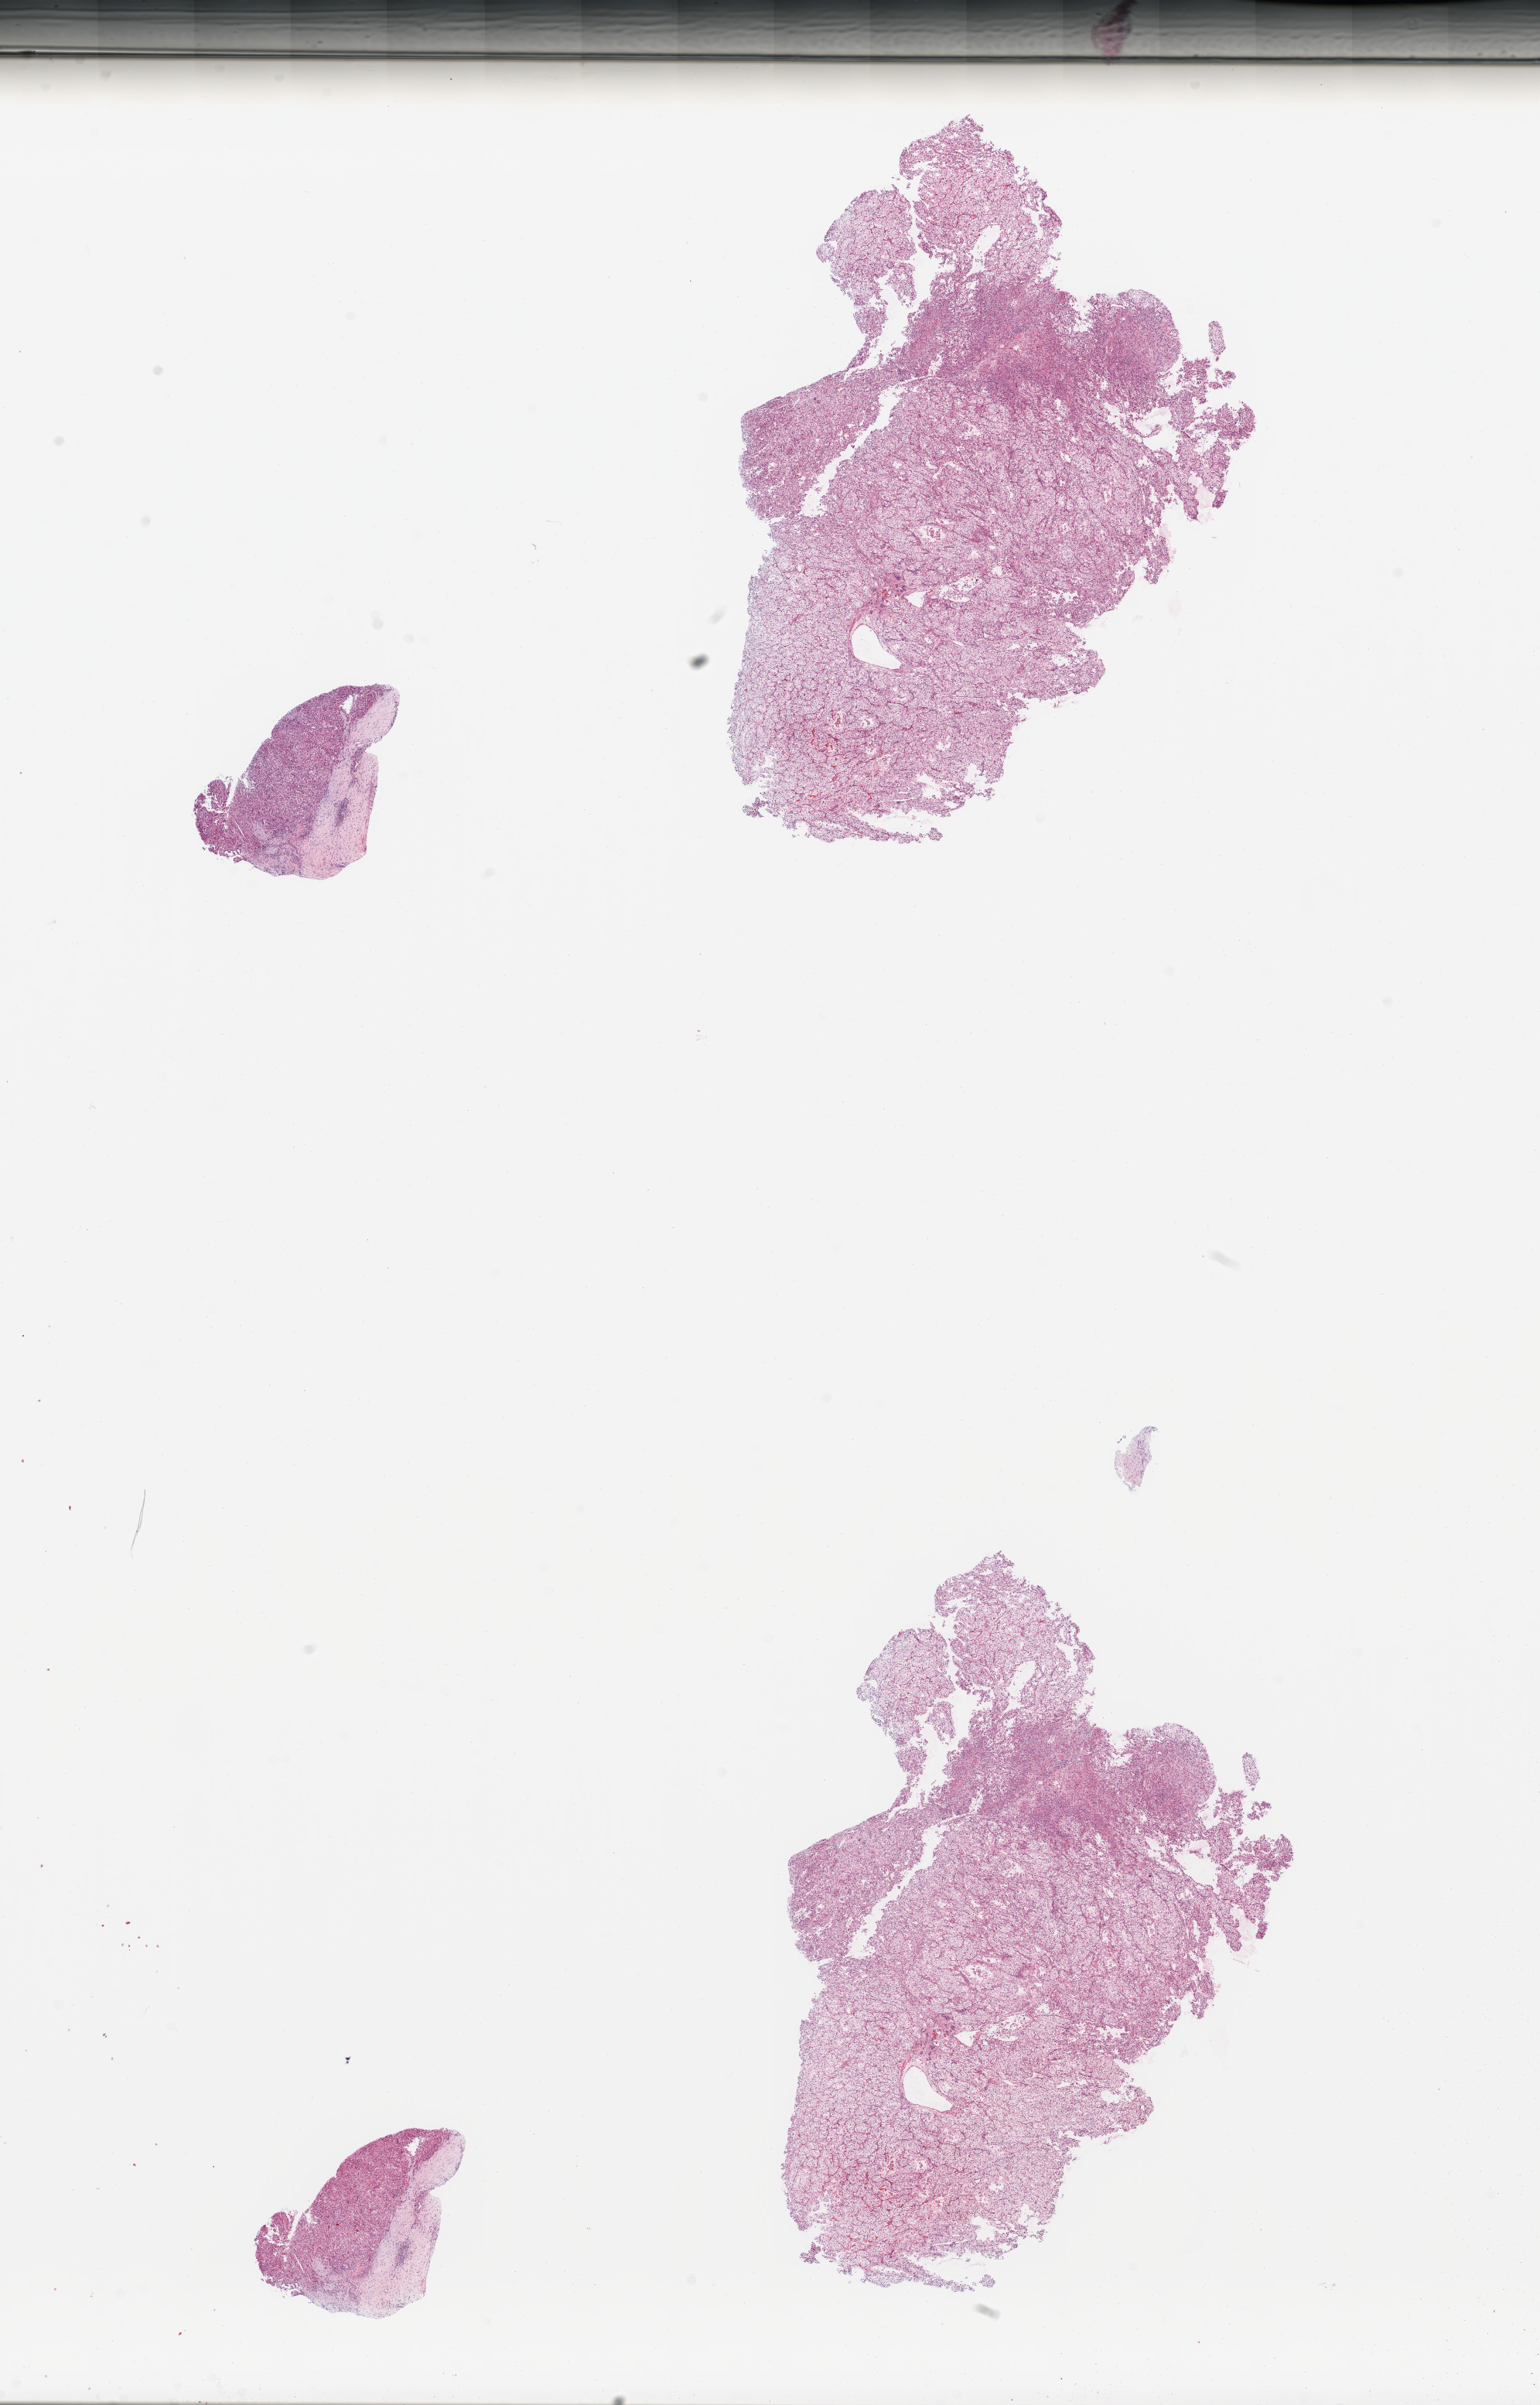
Whole-slide histology image, H&E-stained — shown as a low-resolution overview of the whole scanned area (about 15.8 x 24.6 mm); tumour tissue sample, kidney. Patient: male, age 69 years. Histologic grade: G4 (undifferentiated).
* AJCC pathologic stage: IV
* primary tumour site (as recorded): middle
* diagnosis: Renal cell carcinoma, NOS